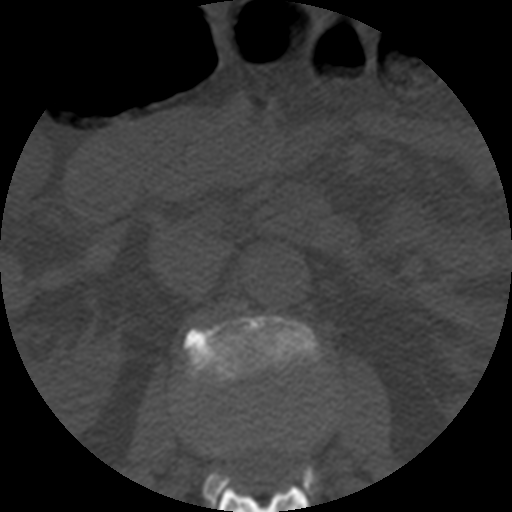
CT including the spine, one axial slice. Bone window (W 1800 / L 400 HU). 512 × 512 image matrix. Patient age 57 years. Case-level facts recorded for this patient, not image findings: primary cancer: prostate.
Structures marked on this image (semi-automatic segmentation, software-assisted and operator-edited):
- L1 vertebra: bounding box (x1, y1, x2, y2) in pixels: (218, 481, 309, 512)
- L2 vertebra: (183, 315, 320, 507)